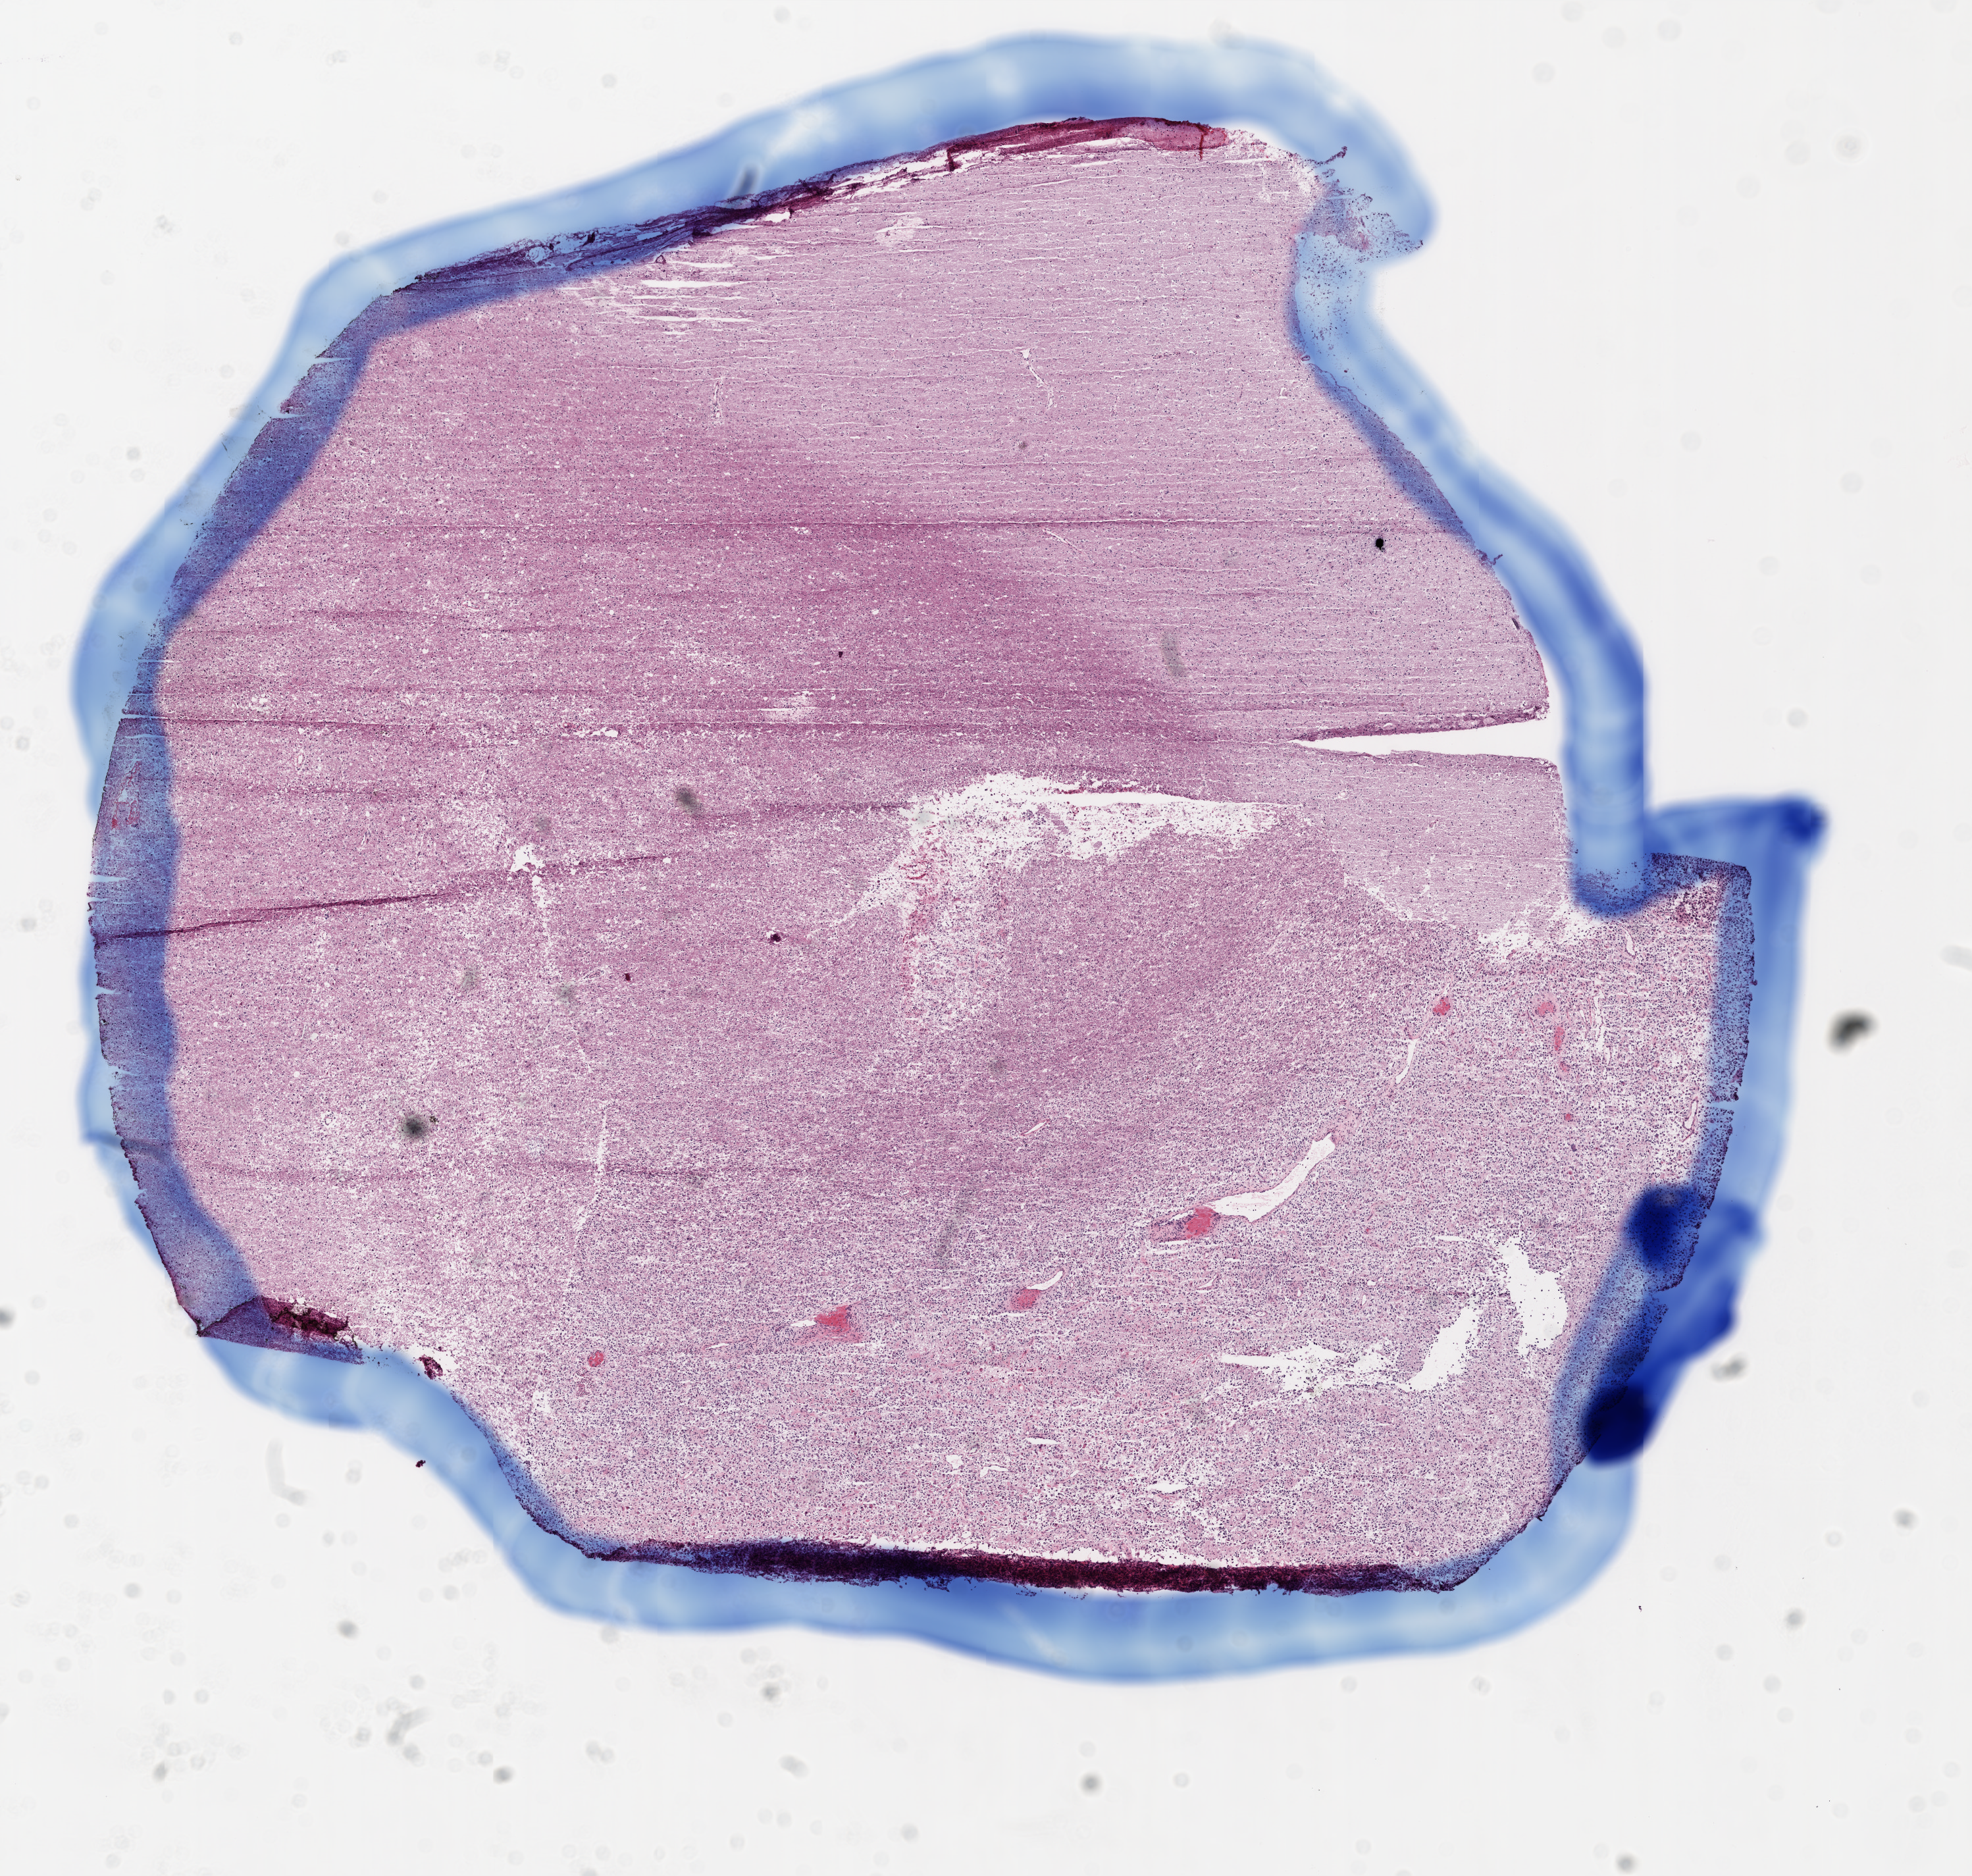
Hematoxylin and eosin (H&E) stained whole-slide image — a low-resolution overview of the entire scanned area, about 12.0 x 11.4 mm; frozen section; brain, primary tumour sample. Male, age 63 years at initial diagnosis. Pathologist review of this section (percent, as recorded): tumour cells 75%, tumour nuclei 95%, normal cells 0%, stromal cells 20%, necrosis 5%.
* diagnosis: Glioblastoma